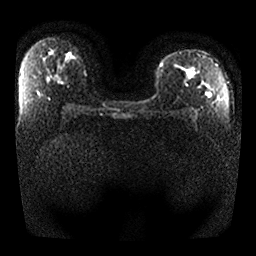
Breast MRI, one axial slice. Slice 15 of 25 in the series (ordered by position). Diffusion-weighted series; image 2 of 4 stored at this slice position (different b-values; order by instance number). 1.5 T. 4 mm slice thickness. 256 × 256 image matrix, field of view 330 × 330 mm. Female patient.
Structures marked on this image (manually delineated by an expert):
- tumour on diffusion-weighted imaging: bounding box [x1, y1, x2, y2] px = [186, 67, 212, 99]